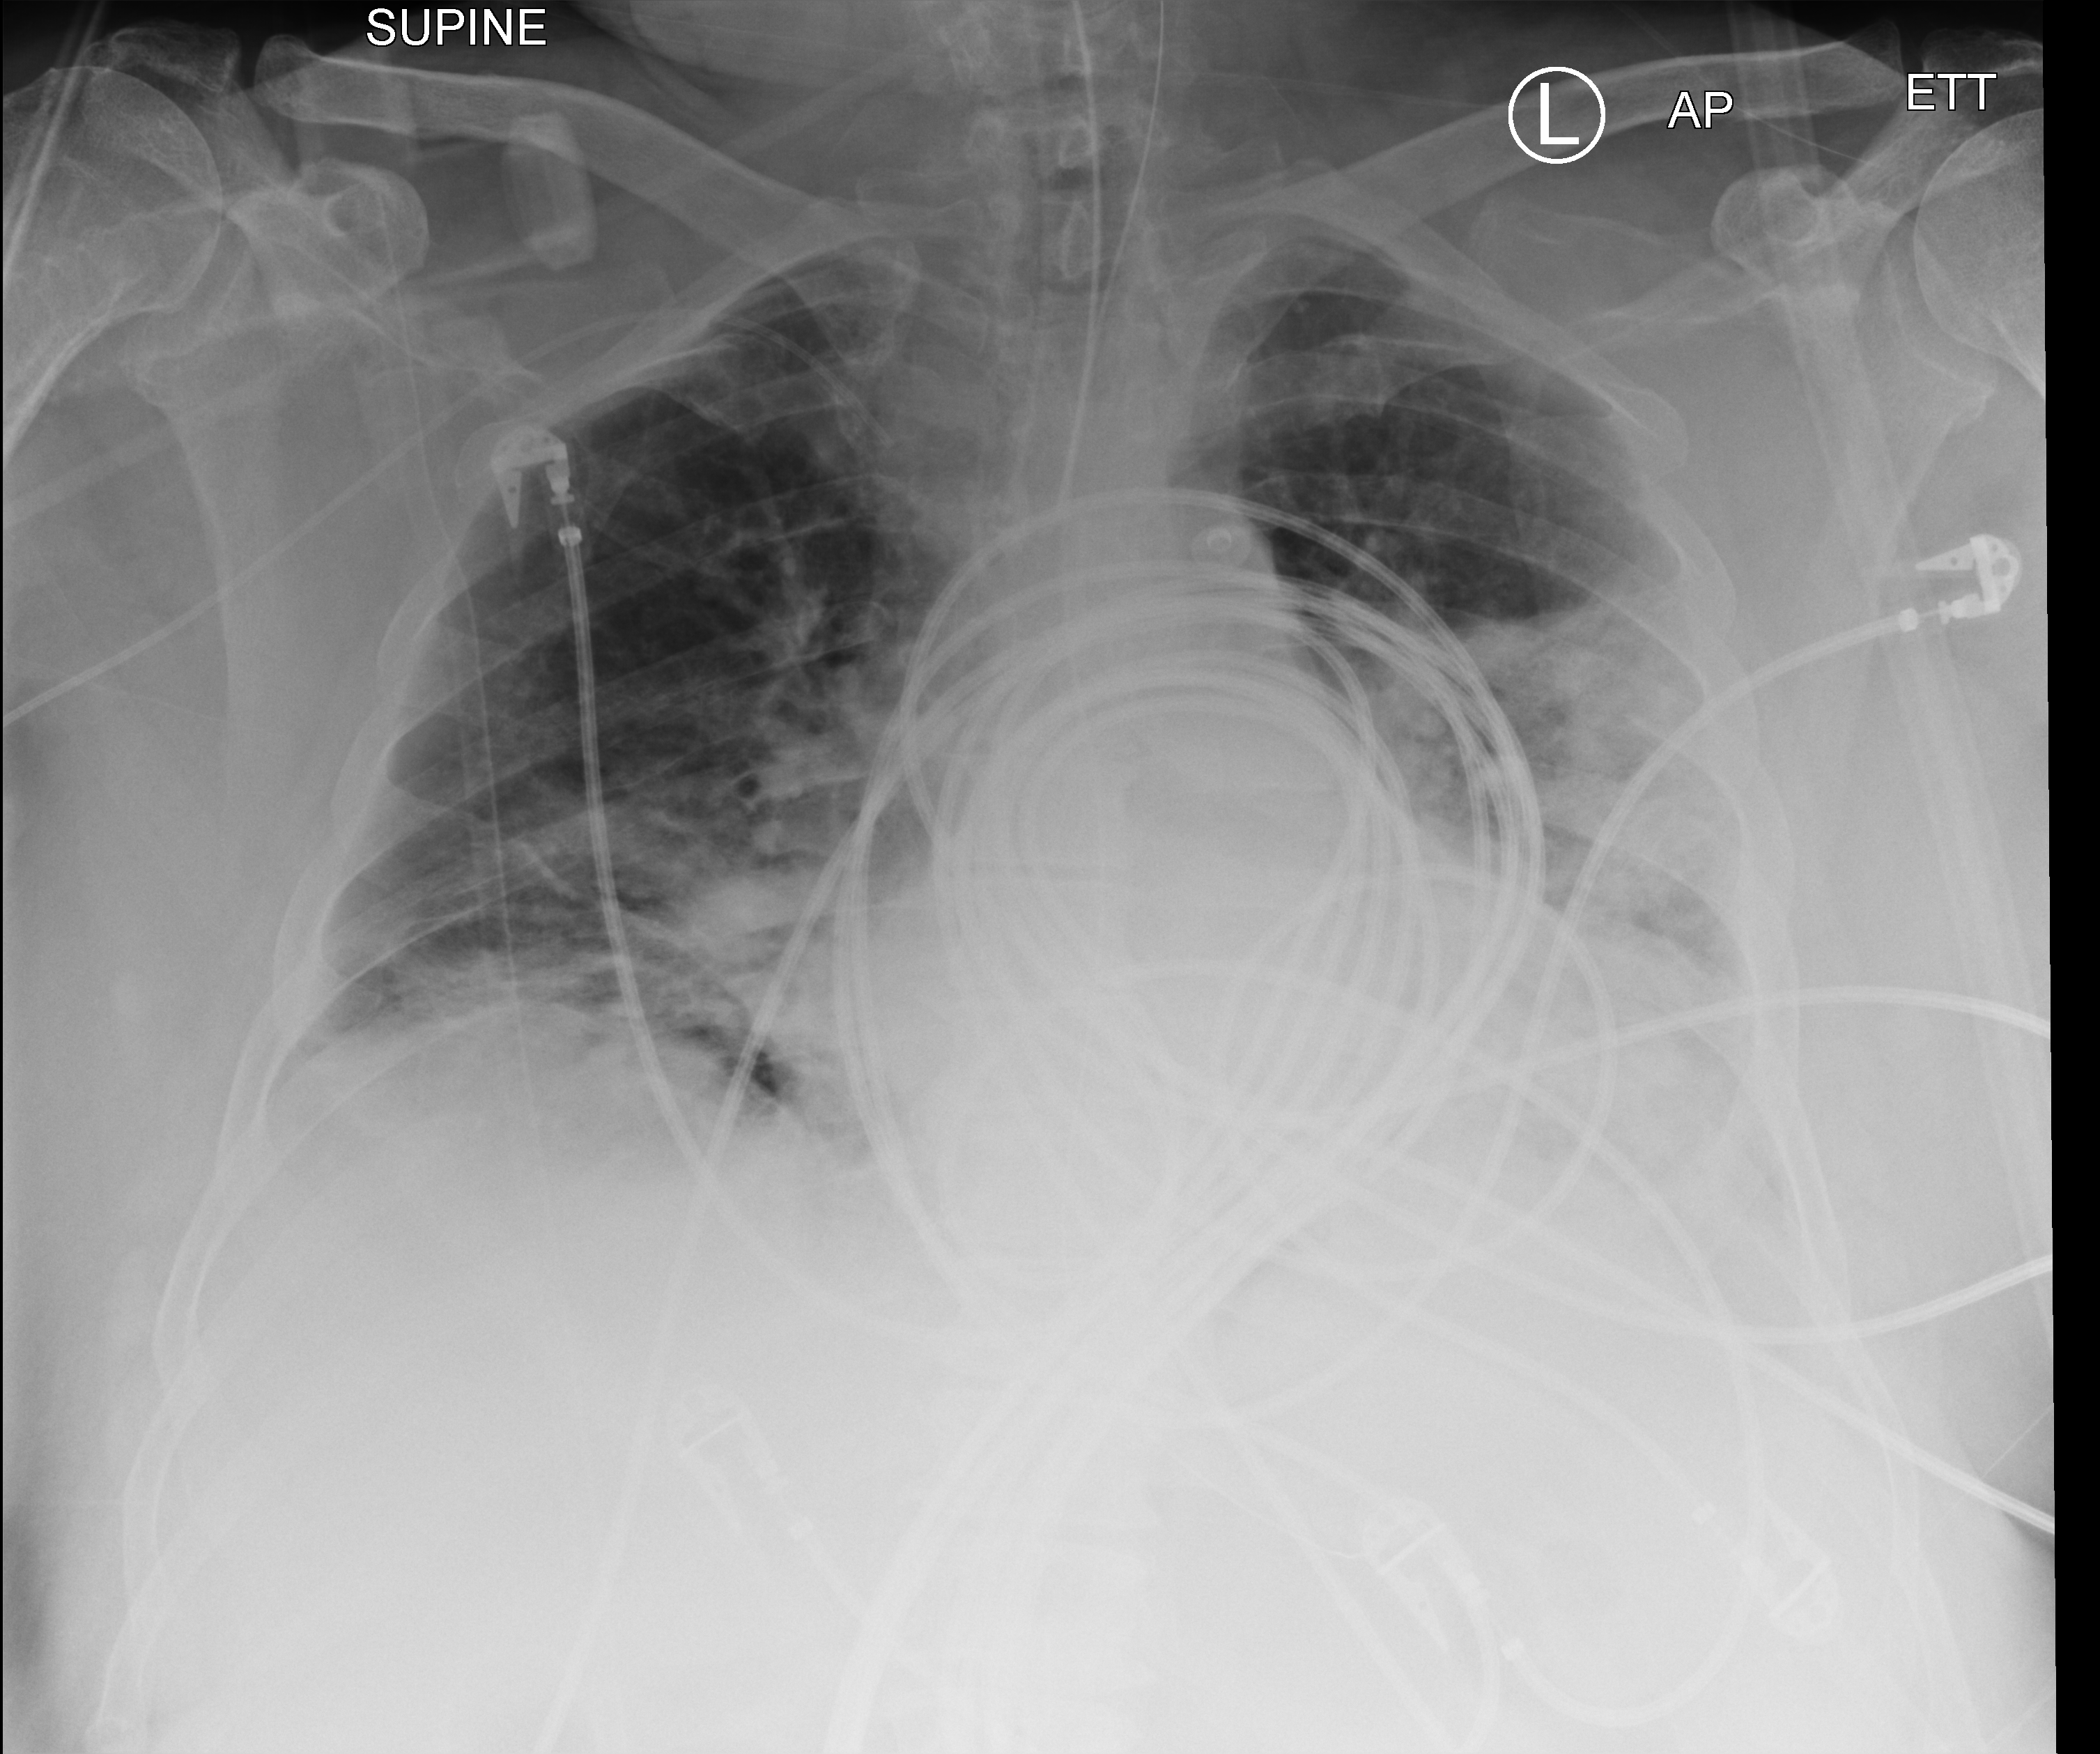
Bedside chest radiograph (computed radiography); anteroposterior (AP) projection. Patient hospitalised with COVID-19; male, aged 60–74 years.
Admission-level facts for this patient (not findings on this image; timing relative to this image not recorded): admitted to intensive care during this hospital stay: yes; length of hospital stay: 26 days; mechanically ventilated during this hospital stay: yes.